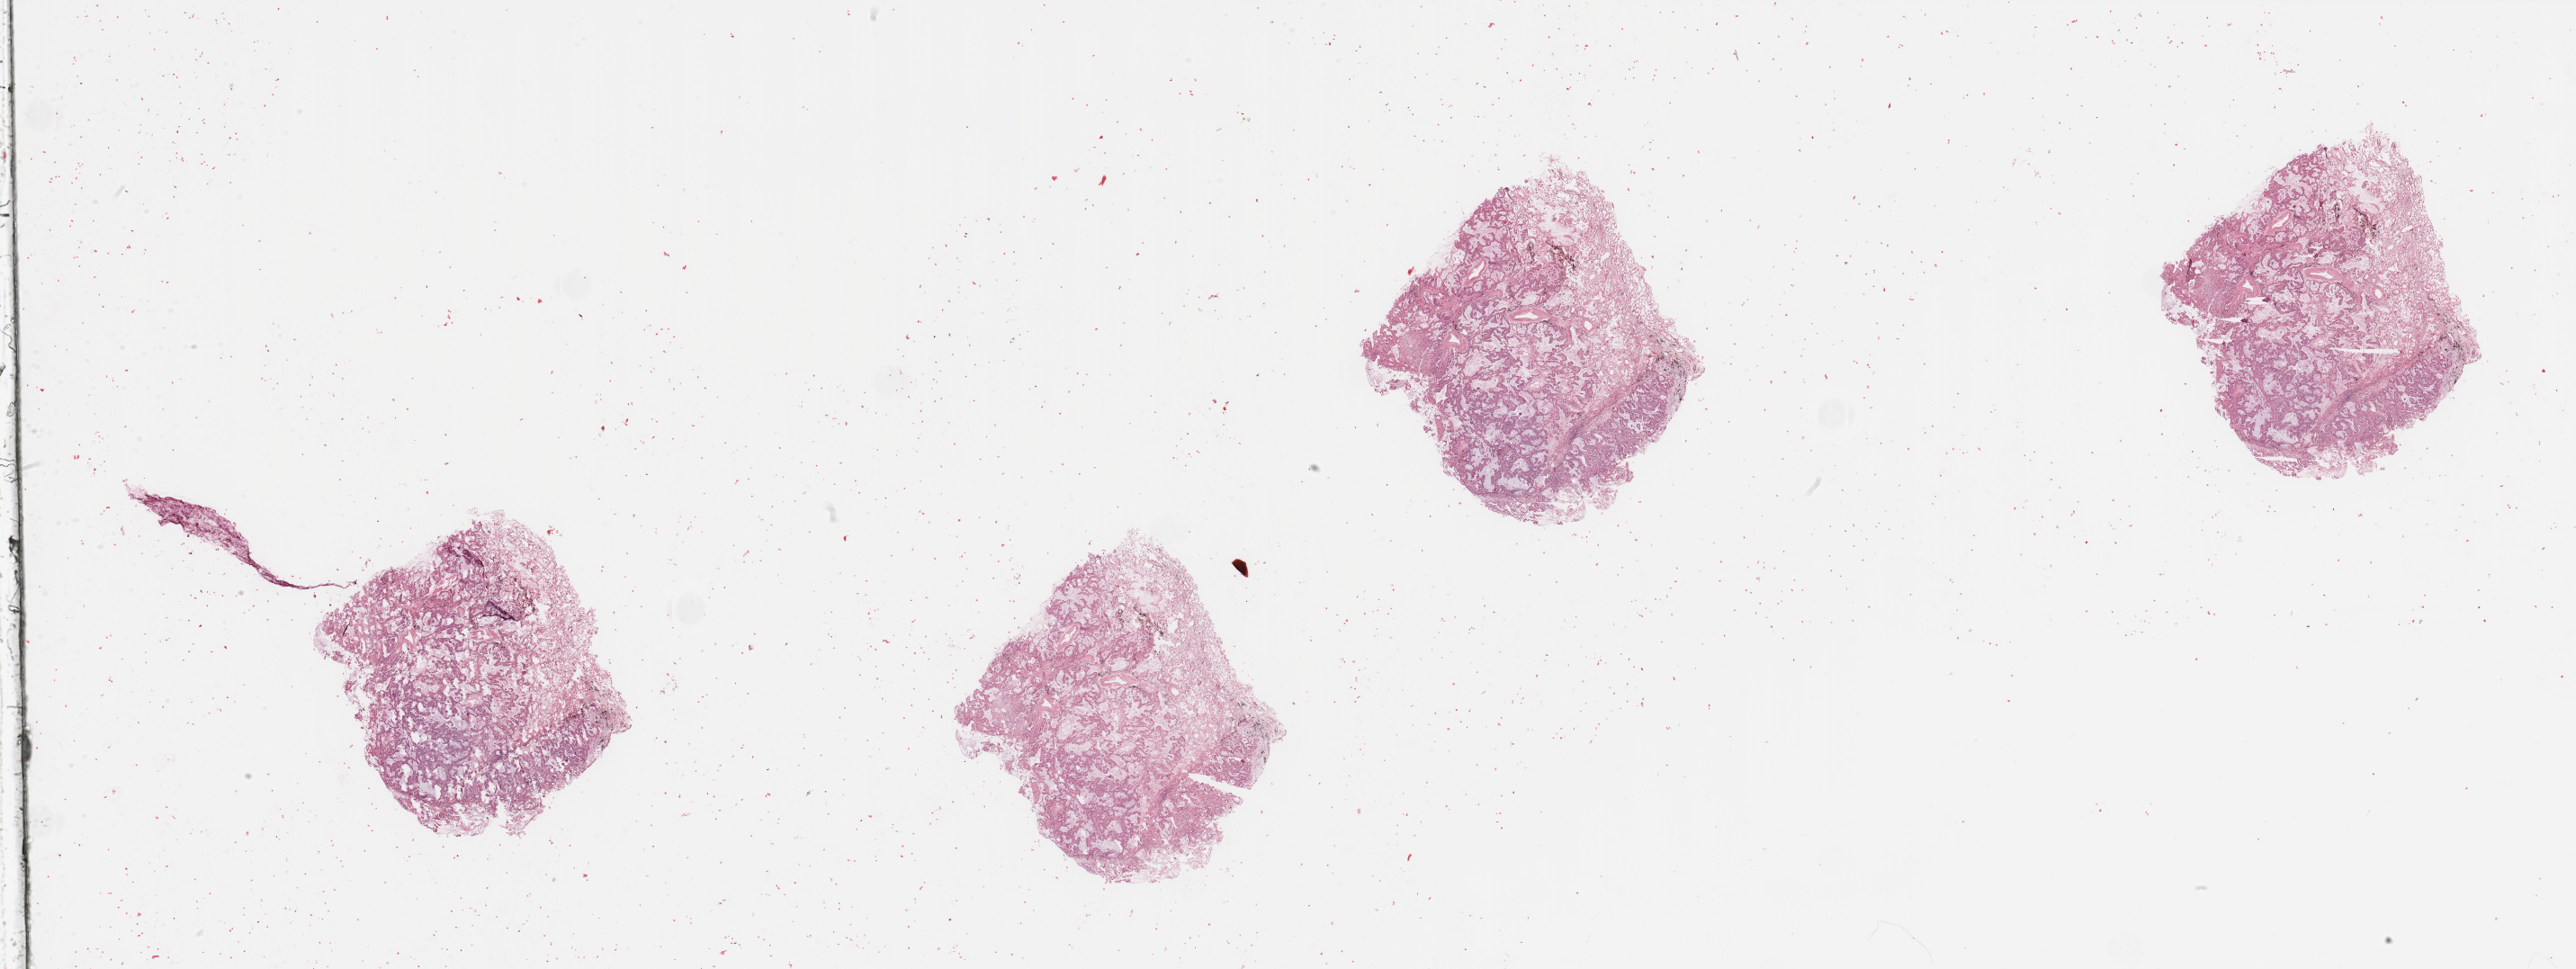
Digitized H&E tissue section (whole slide), whole scanned area (about 45.3 x 17.0 mm, acquisition: 20x scan) shown as a low-resolution overview; tumour tissue sample, sampled site: lung. Male, 69 y/o. Histologic grade: G2 (moderately differentiated). Pathologist review of this section (percent, as recorded): tumour nuclei 70%, necrosis 5%.
AJCC pathologic stage: IA. Histologic diagnosis: Adenocarcinoma, NOS. Primary tumour site (as recorded): right upper lobe.